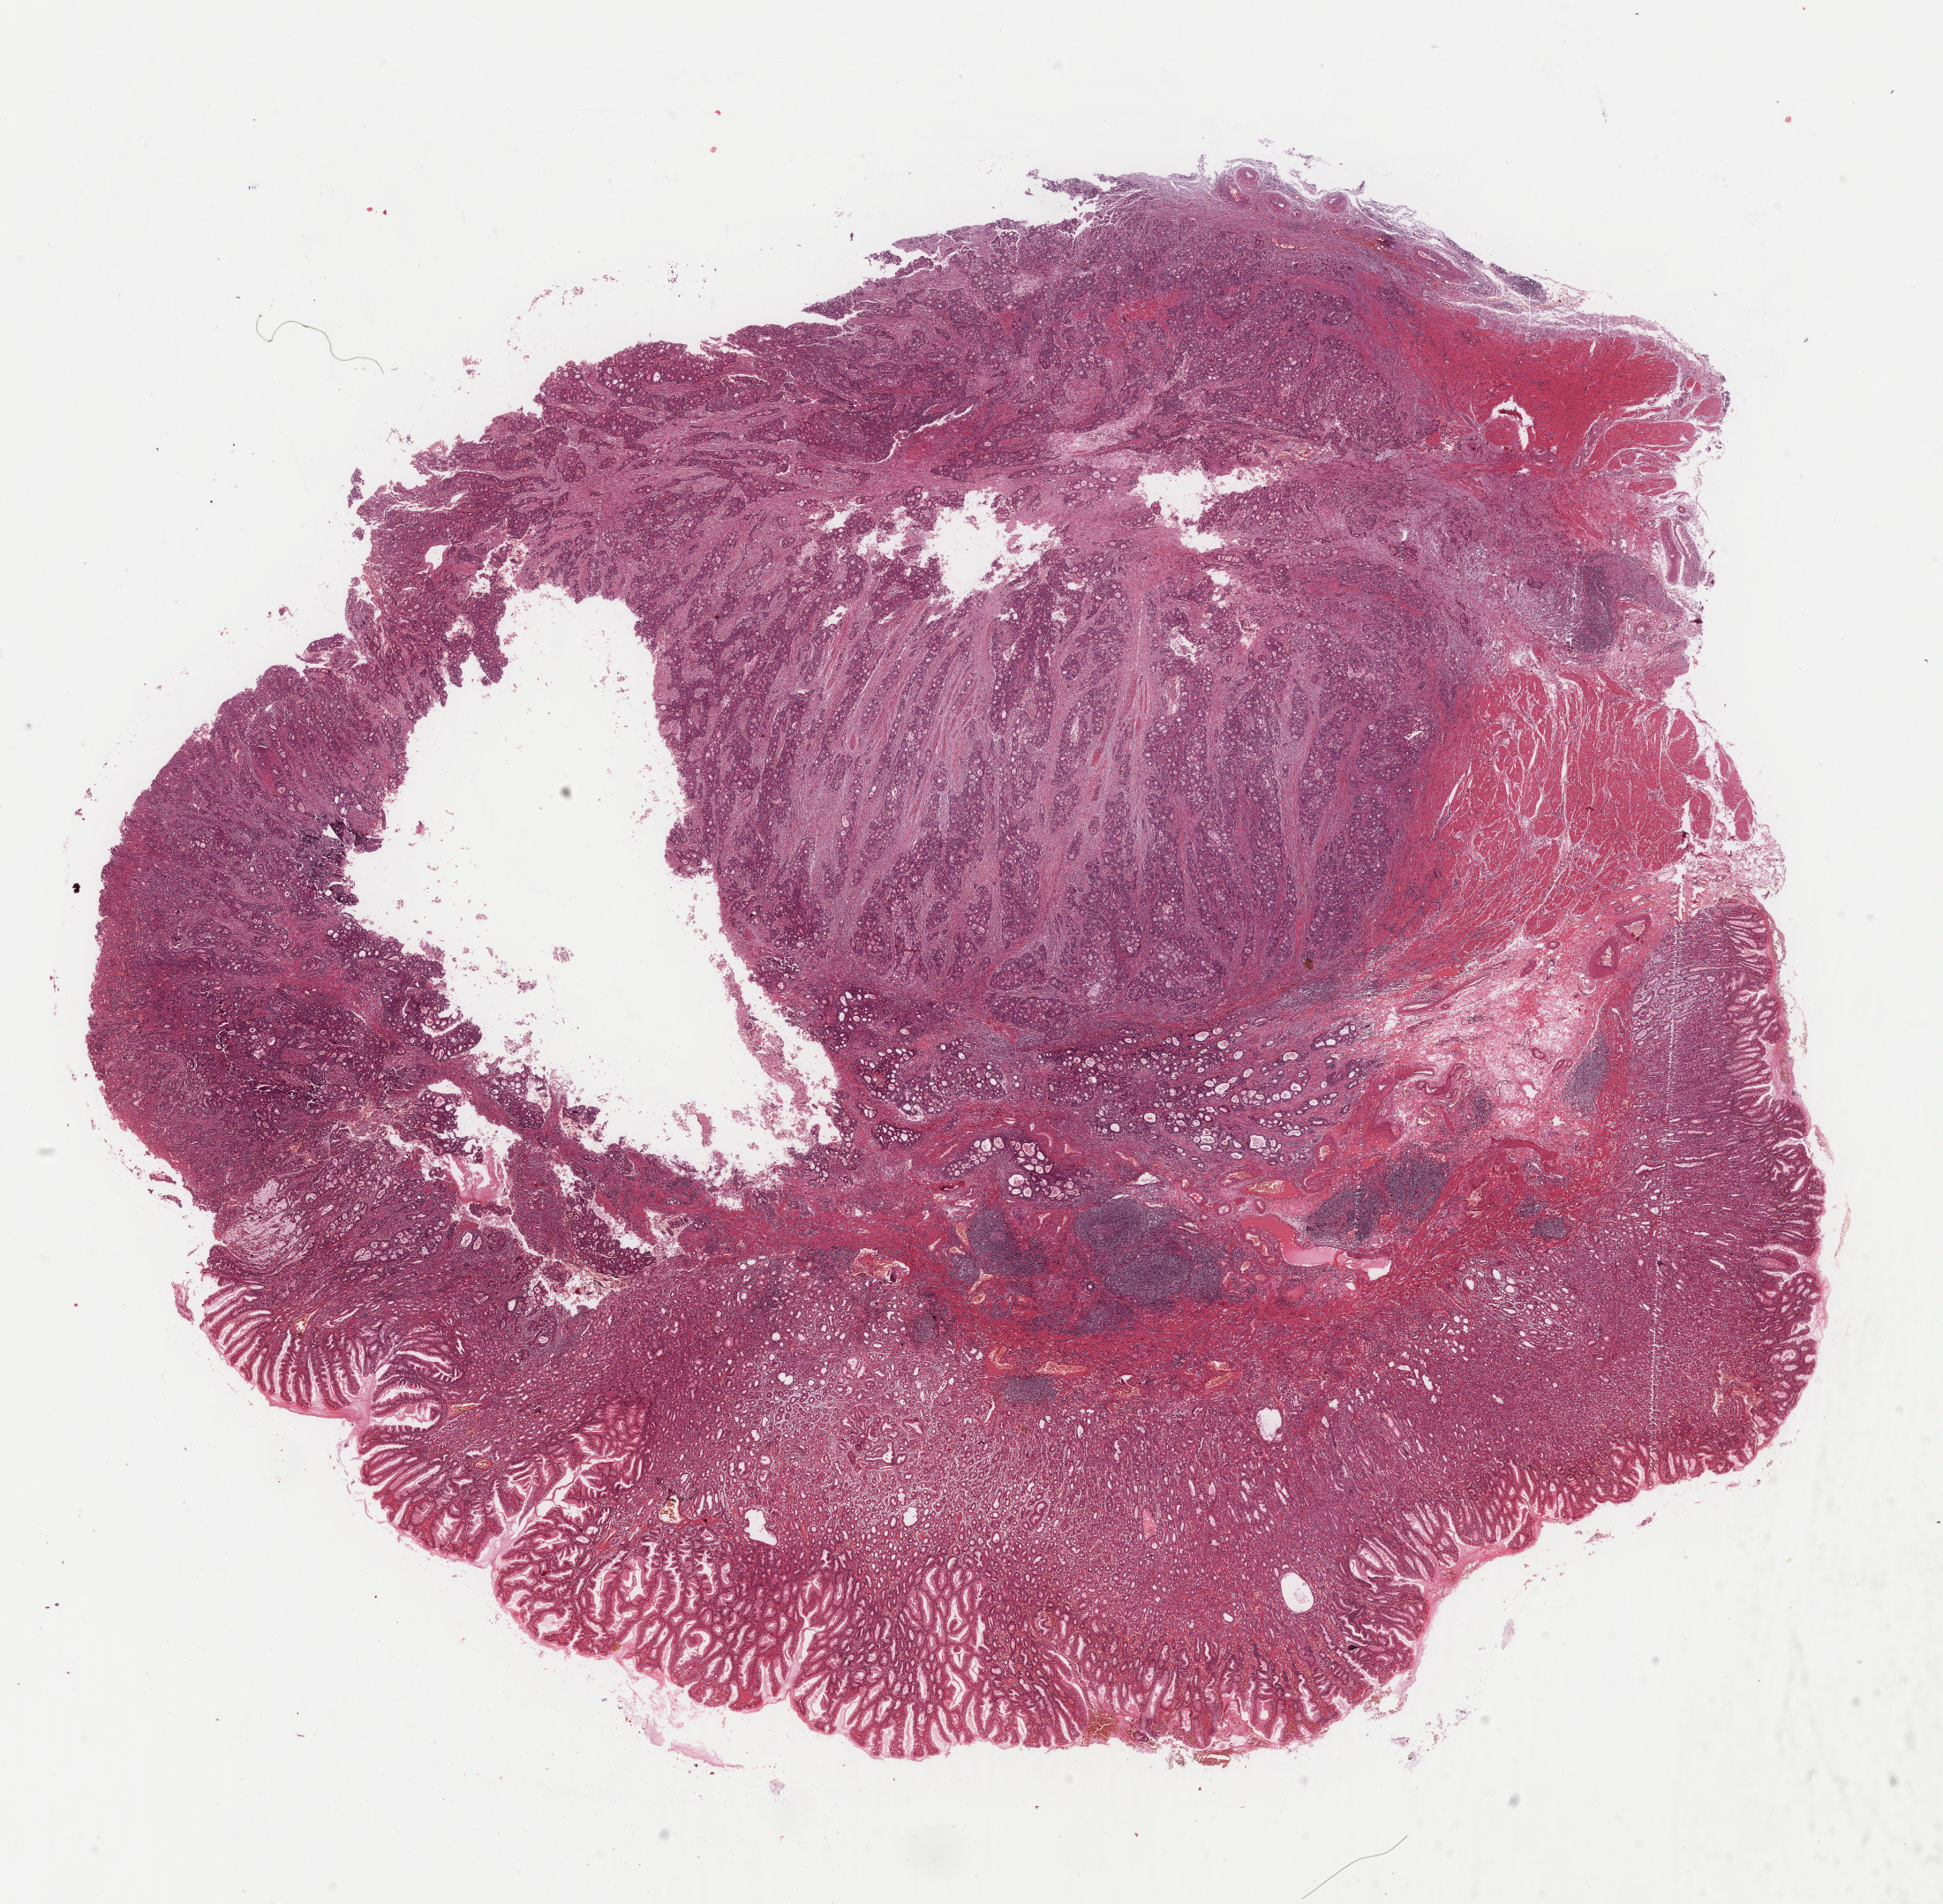
Whole-slide histology image, H&E-stained — shown as a low-resolution overview of the whole scanned area (about 17.5 x 17.1 mm, from a 40x scan). Formalin-fixed paraffin-embedded (FFPE) diagnostic section. Sample: primary tumour, stomach. Male, age 57 years at initial diagnosis. Histologic grade: G2 (moderately differentiated).
* histologic diagnosis: Adenocarcinoma, NOS (cardia, NOS)
* AJCC pathologic stage: IIA